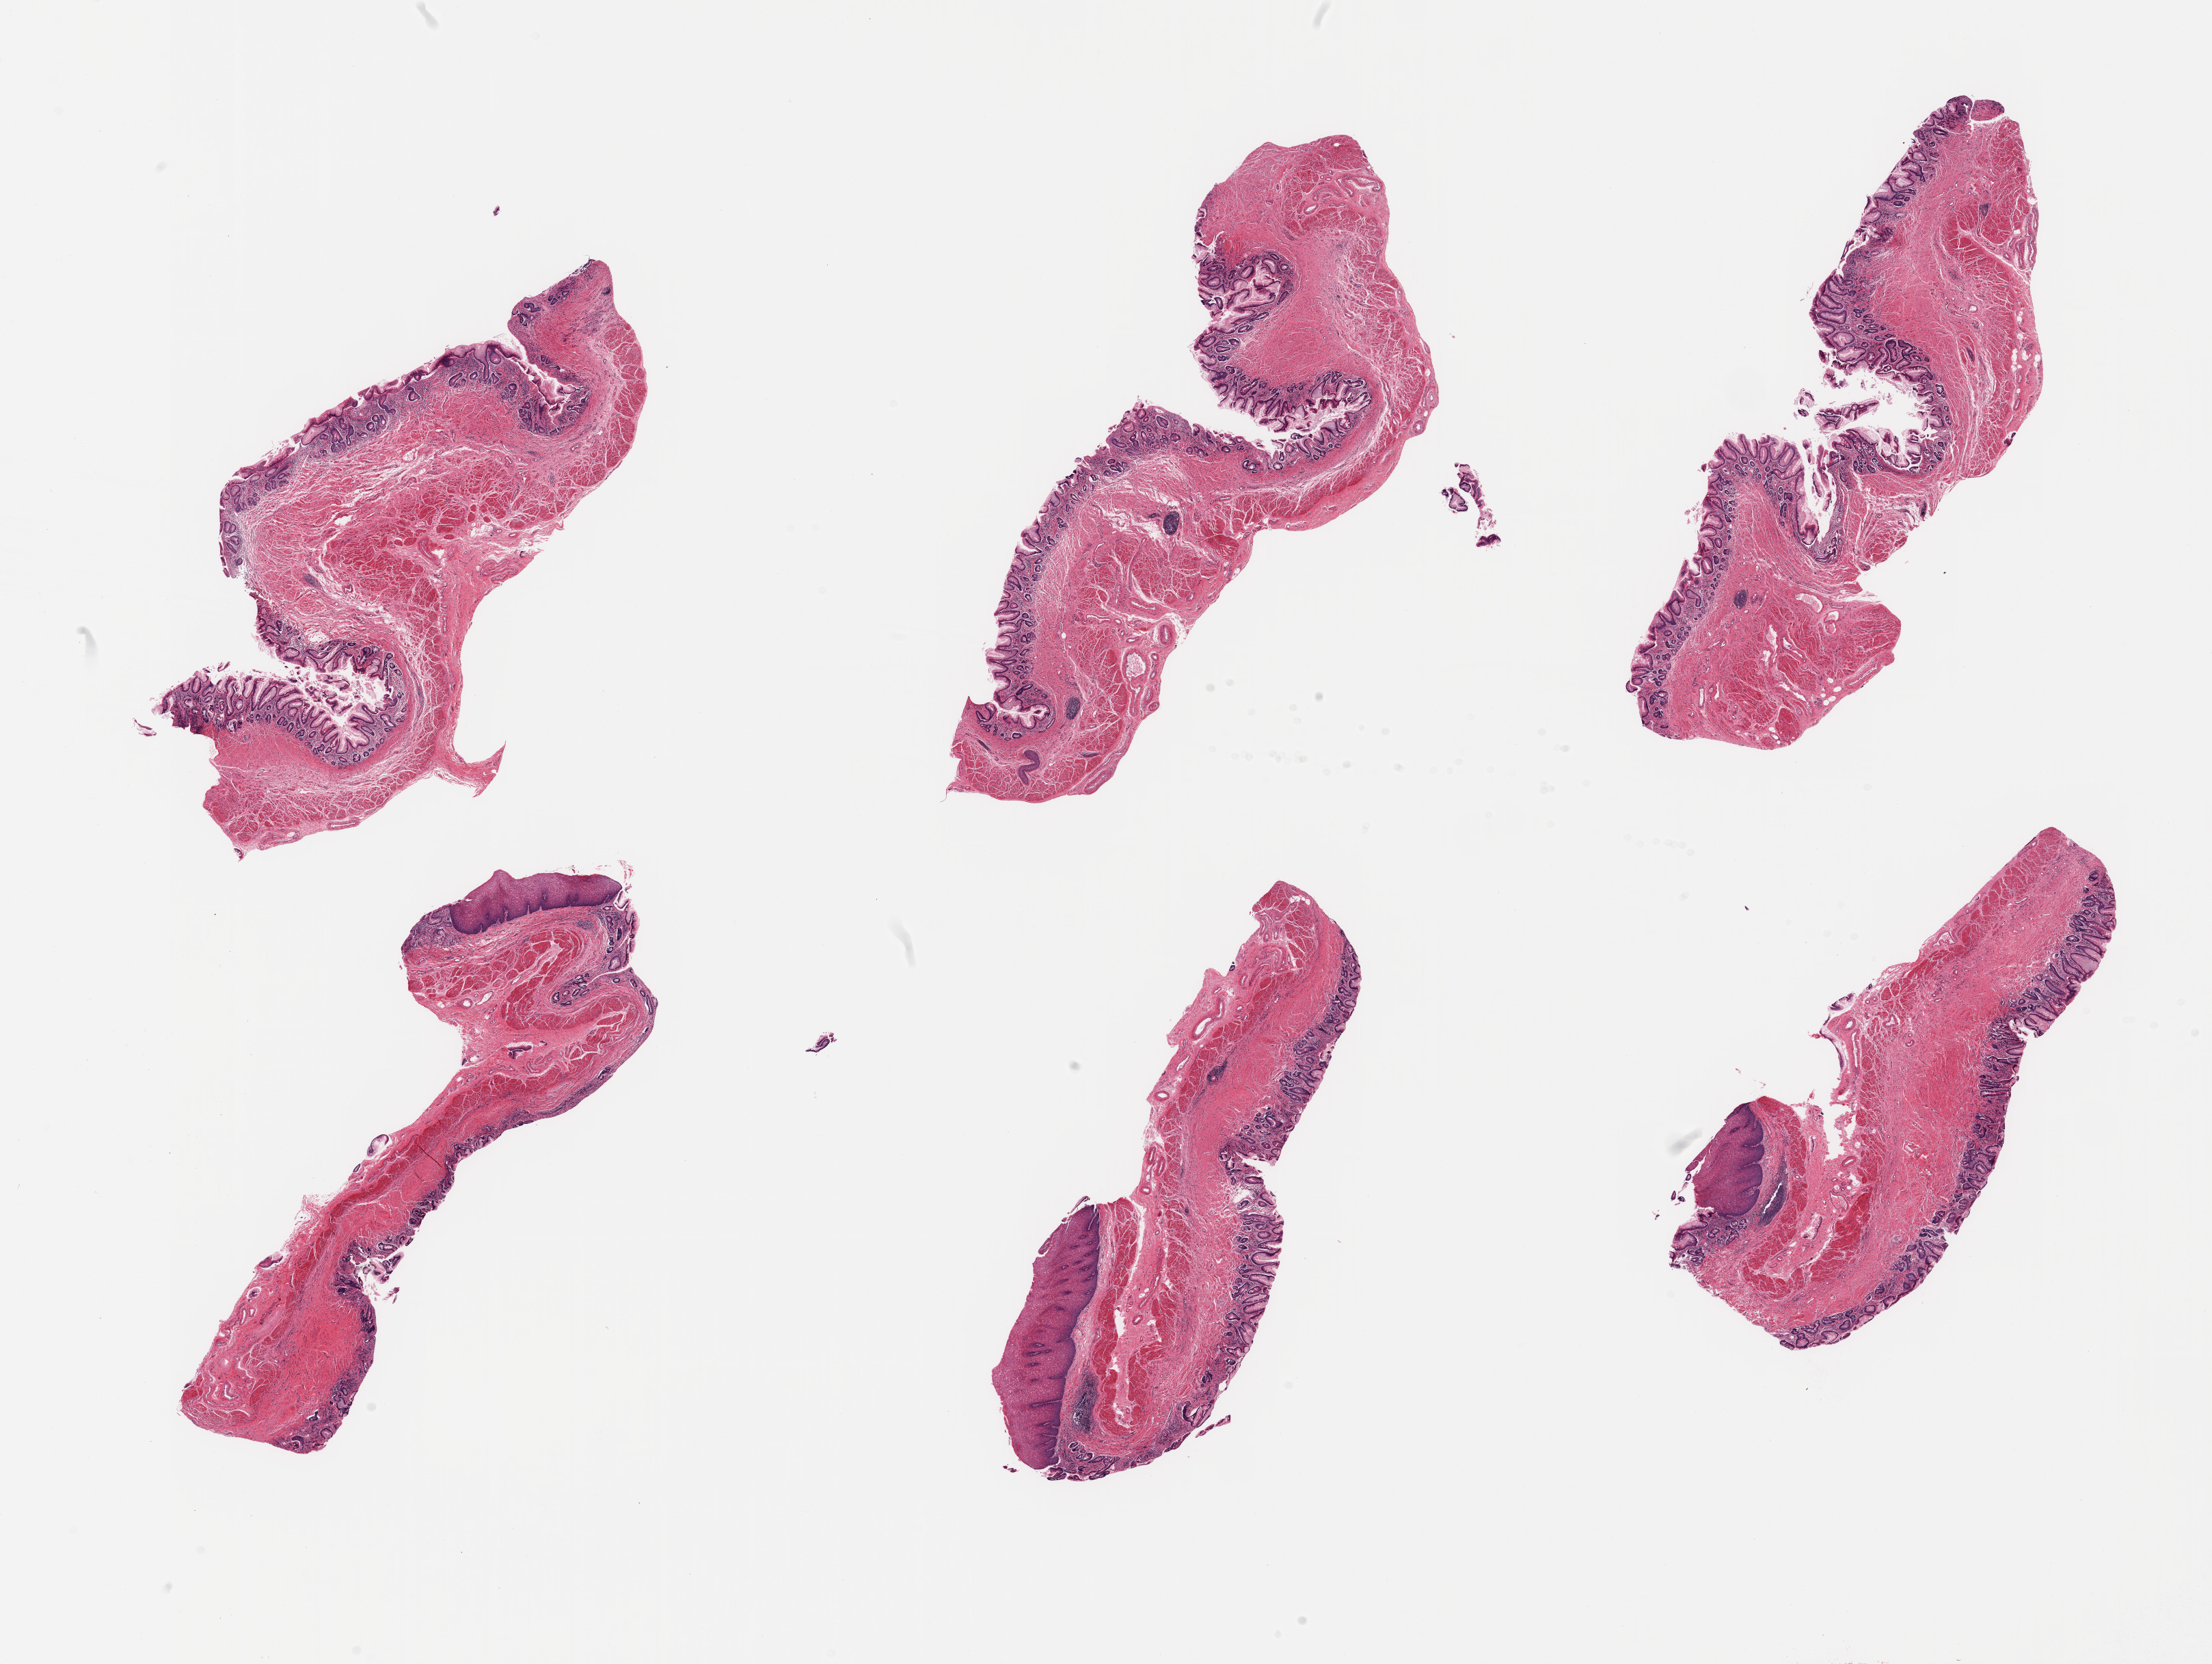
Whole-slide image, haematoxylin and eosin stain, whole scanned area (about 25.6 x 19.3 mm, slide scanned at 20x) shown as a low-resolution overview, PAXgene-fixed paraffin-embedded (PFPE) section, target tissue: esophageal mucous membrane, tissue donor sample. Donor: female.
Pathologist's review note for this sample: 6 pieces; squamous & glandular mucosa with intestinal metaplasia (Barrett esophagus) no dysplasia.